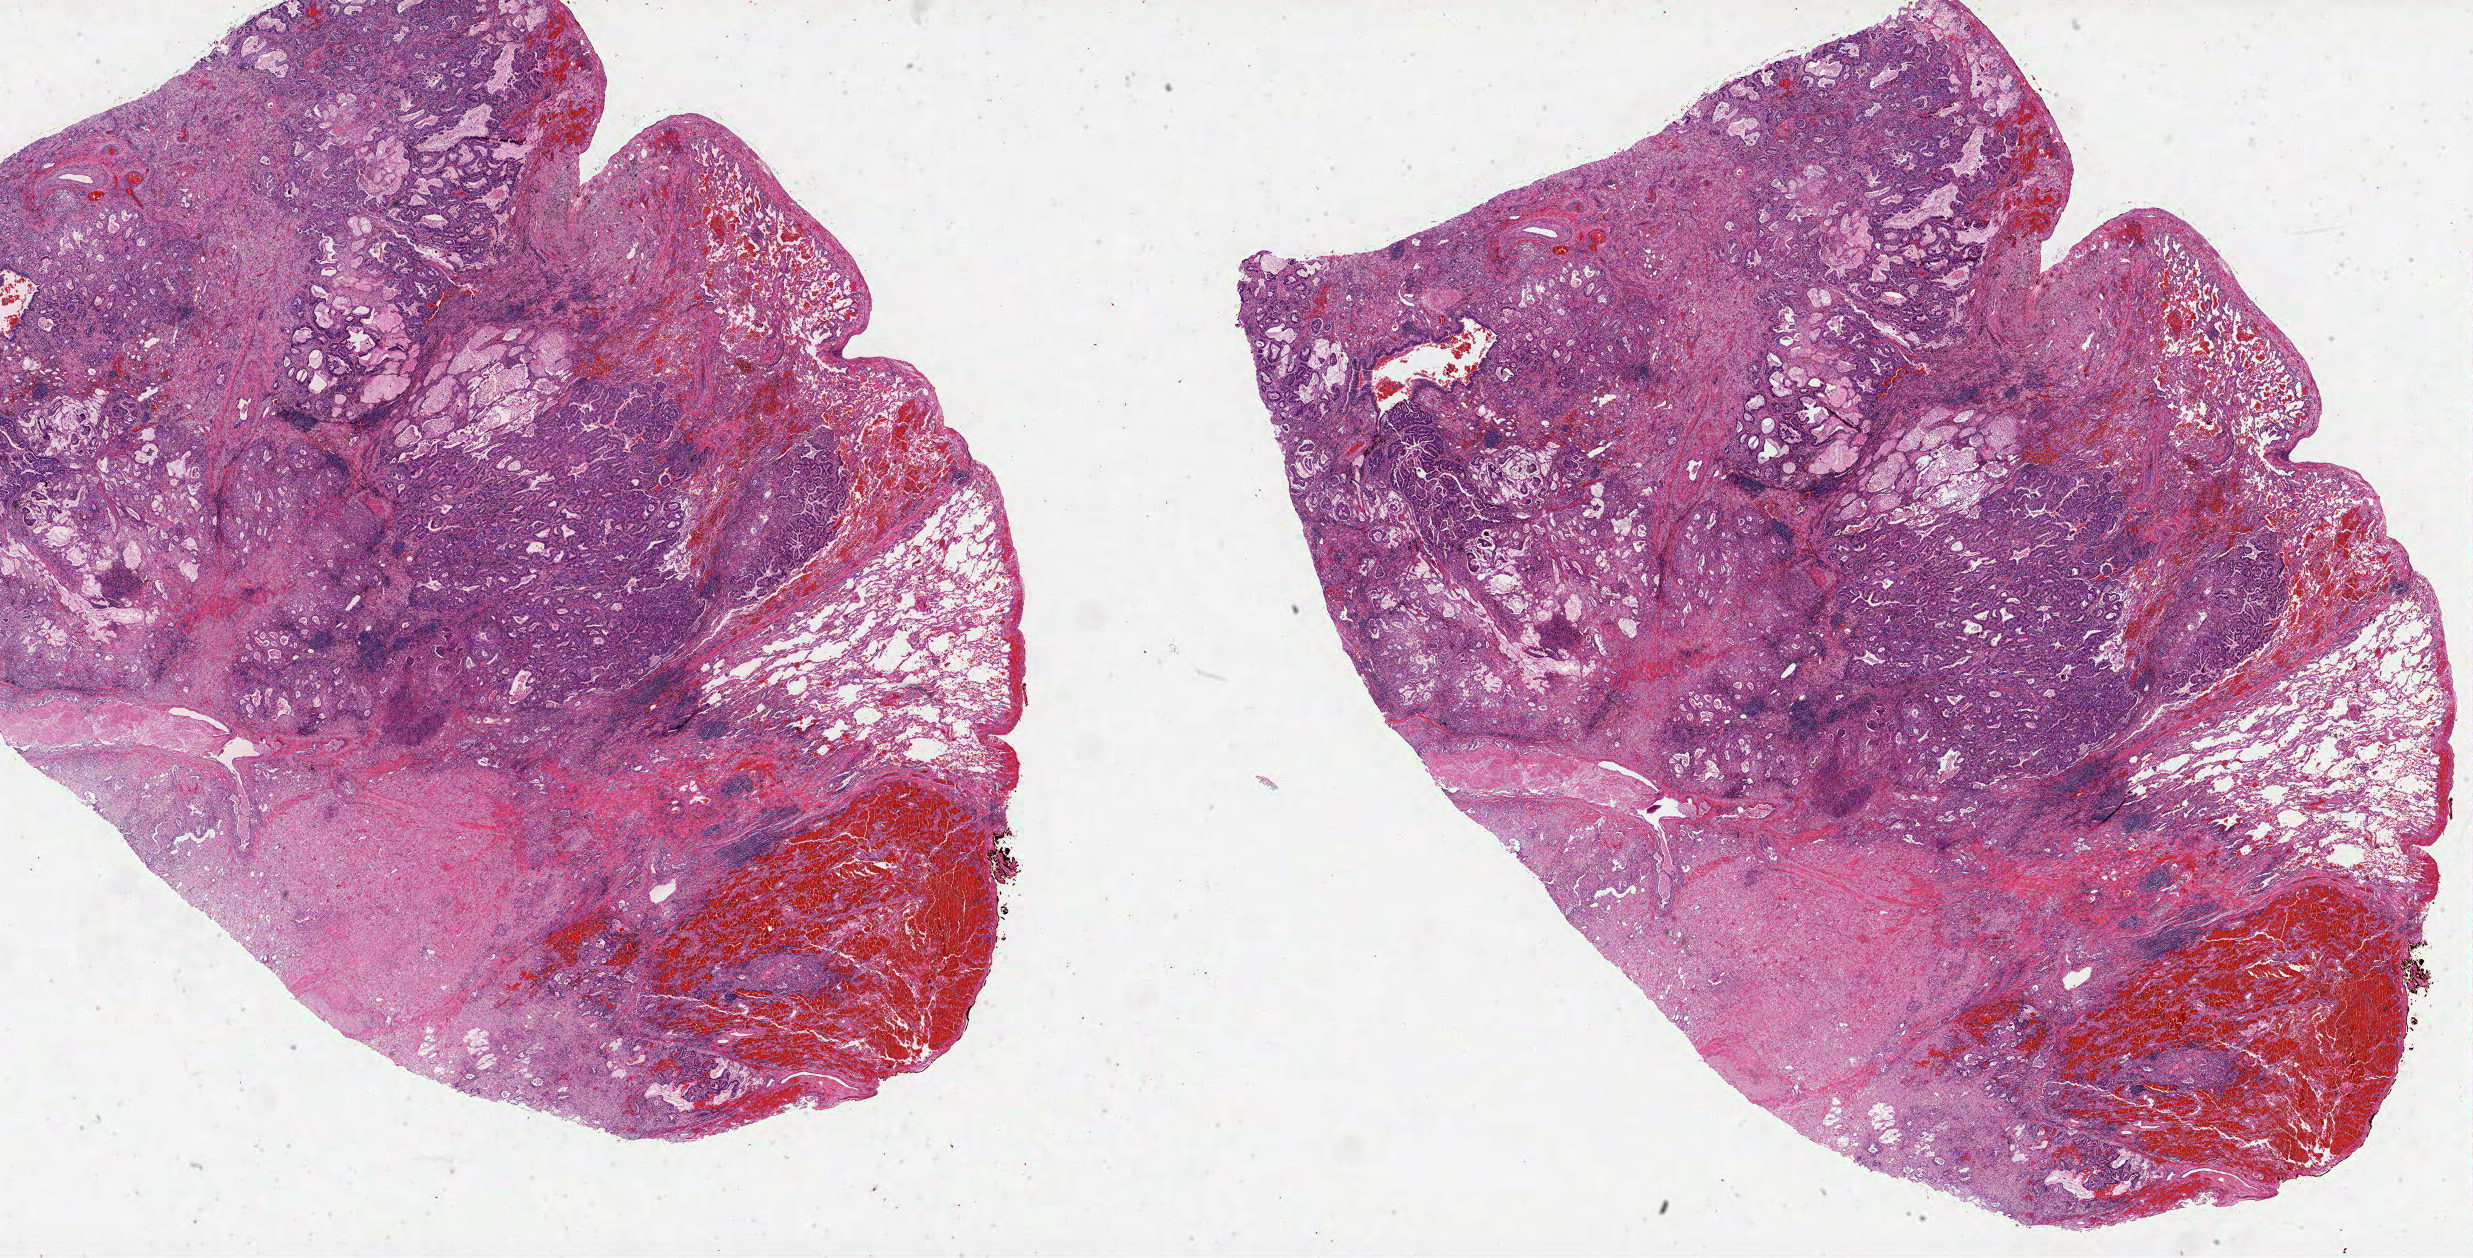
Whole-slide histology image, H&E-stained, a low-resolution overview of the entire scanned area, about 39.9 x 20.3 mm; FFPE section; lung, primary tumour sample. Male, age 70 years at initial diagnosis.
• AJCC pathologic stage: IIA
• laterality: left
• diagnosis: Mucinous adenocarcinoma